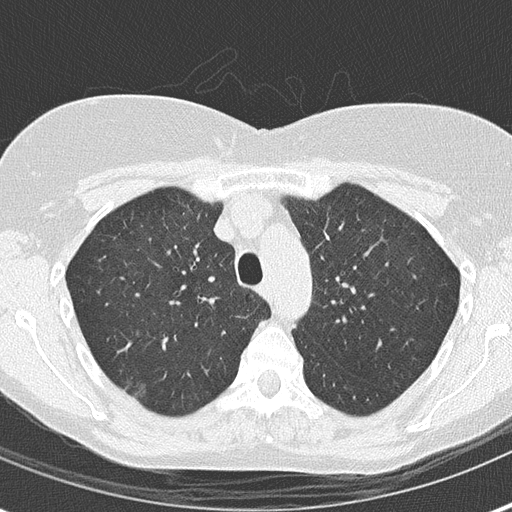
Low-dose screening chest CT, axial slice, baseline screening round, lung window (W 1500 / L -600 HU). Female participant, aged 56 years at enrolment. Current smoker at enrolment.
- Expert-annotated lung lesion, bounding box [x1, y1, x2, y2] px = [109, 358, 163, 411].
- The screening reader recorded 2 non-calcified nodules or masses ≥4 mm on this exam (right upper lobe, left upper lobe); which of them this box marks is not recorded.
- Official screen result: positive, change unspecified: nodule(s) >= 4 mm or enlarging nodule(s), mass(es), or other non-specific abnormalities suspicious for lung cancer.
- Later outcome: lung cancer diagnosed 457 days after this screen — bronchiolo-alveolar adenocarcinoma, NOS, right upper lobe, well differentiated (G1), stage IA (AJCC 6th edition), 15 mm at pathology.